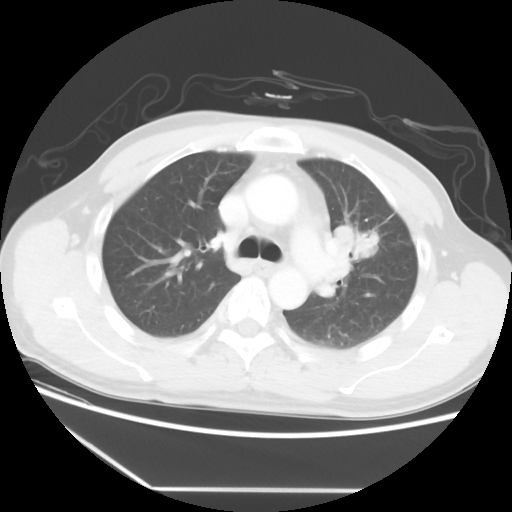
Chest CT, one axial slice. Slice 38 of 56 in the series (ordered by position). Reconstruction kernel STANDARD. Lung window (W 1500 / L -600 HU). 5 mm slice thickness. 512 × 512 image matrix, field of view 373 × 373 mm. Male patient, age 53 years. From the clinical record (not read from this slice): clinical TNM (as recorded): T2a N1 M1b.
Annotated regions visible in this slice (bounding box drawn by a radiologist):
- lung tumour (recorded histology: adenocarcinoma): bounding box (x1, y1, x2, y2) in pixels: (335, 221, 384, 265)